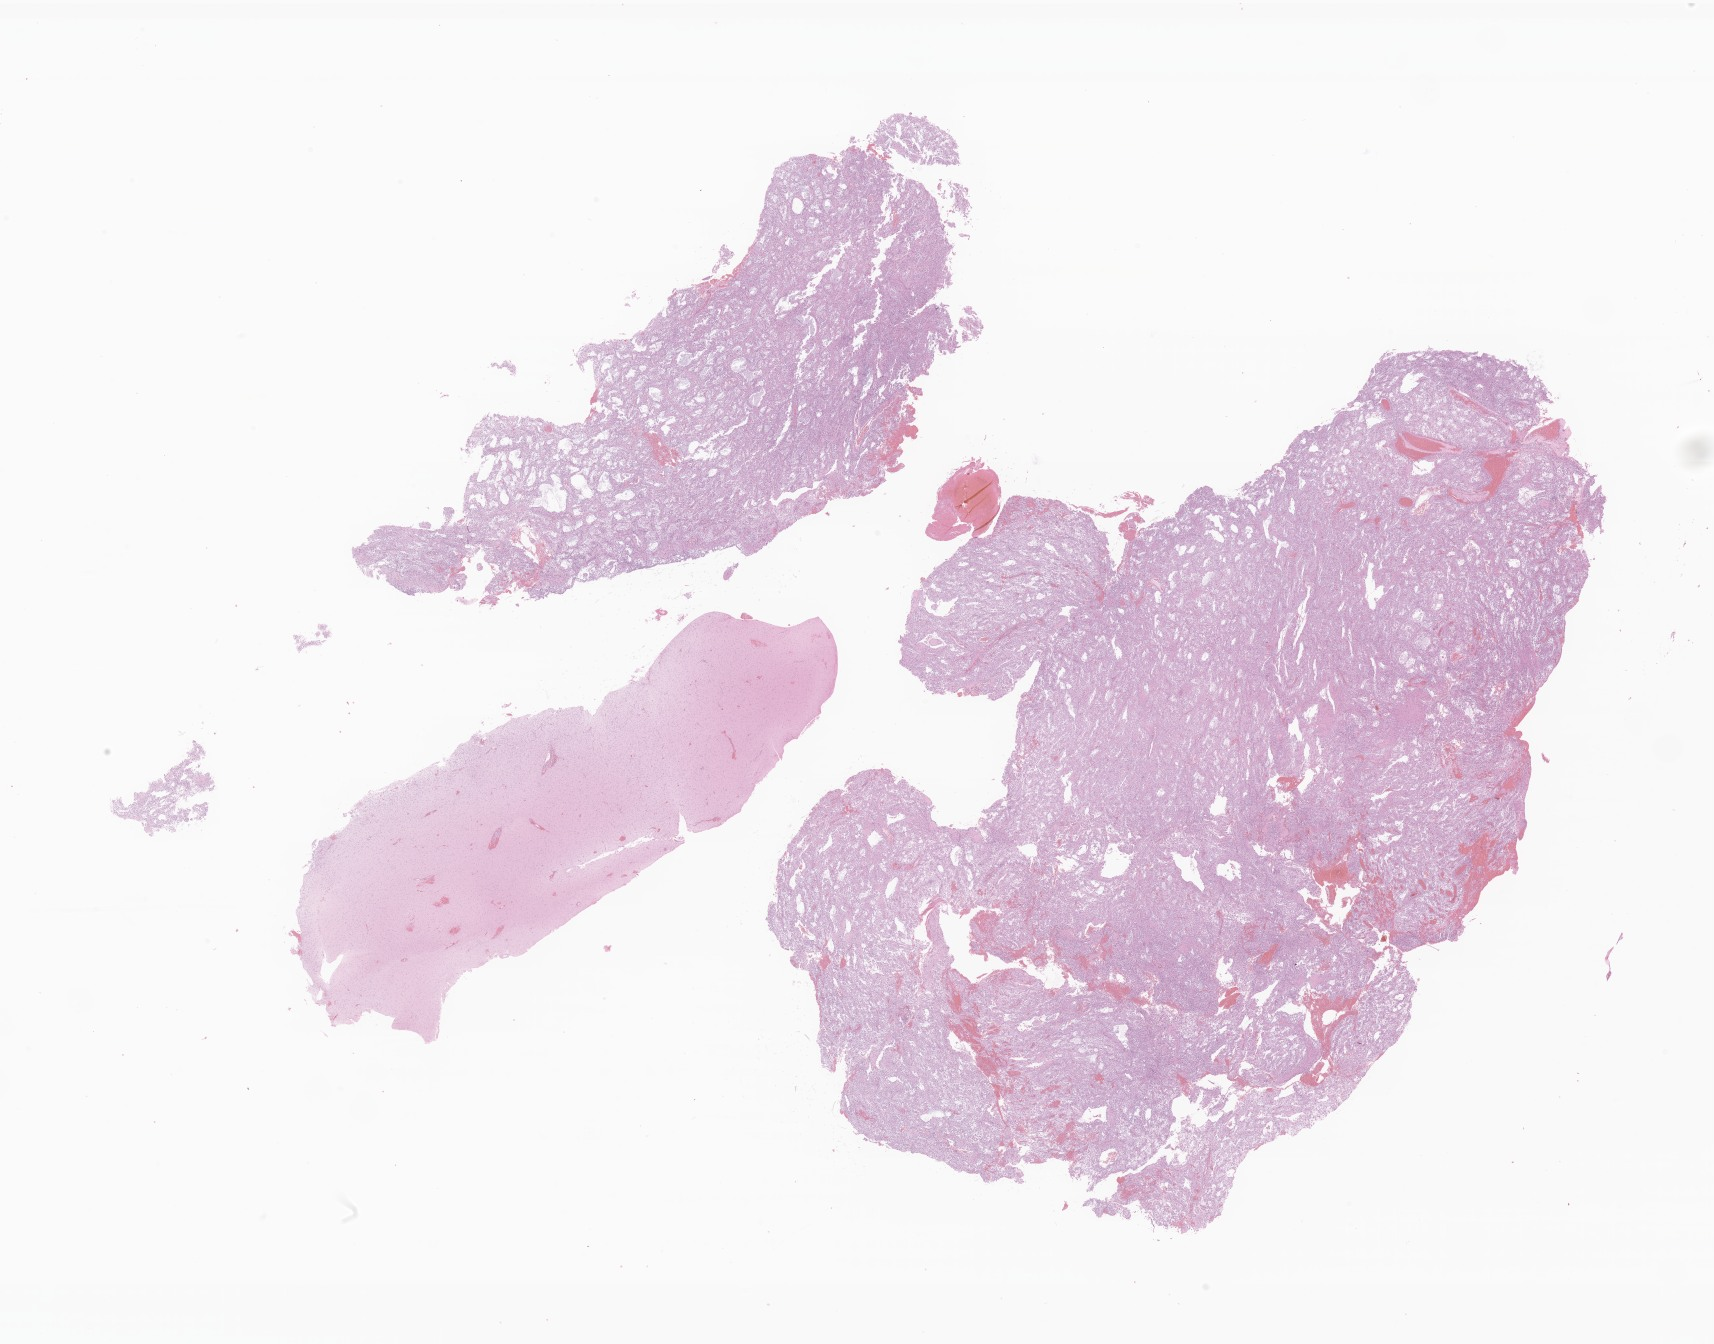
Digitized H&E-stained section of tumor tissue from the cerebellum, low-resolution overview of the scanned area, about 28.9 x 22.7 mm; formalin-fixed paraffin-embedded section. Male patient, age 57 months (4 years 9 months).
* recorded diagnosis: Pilocytic astrocytoma